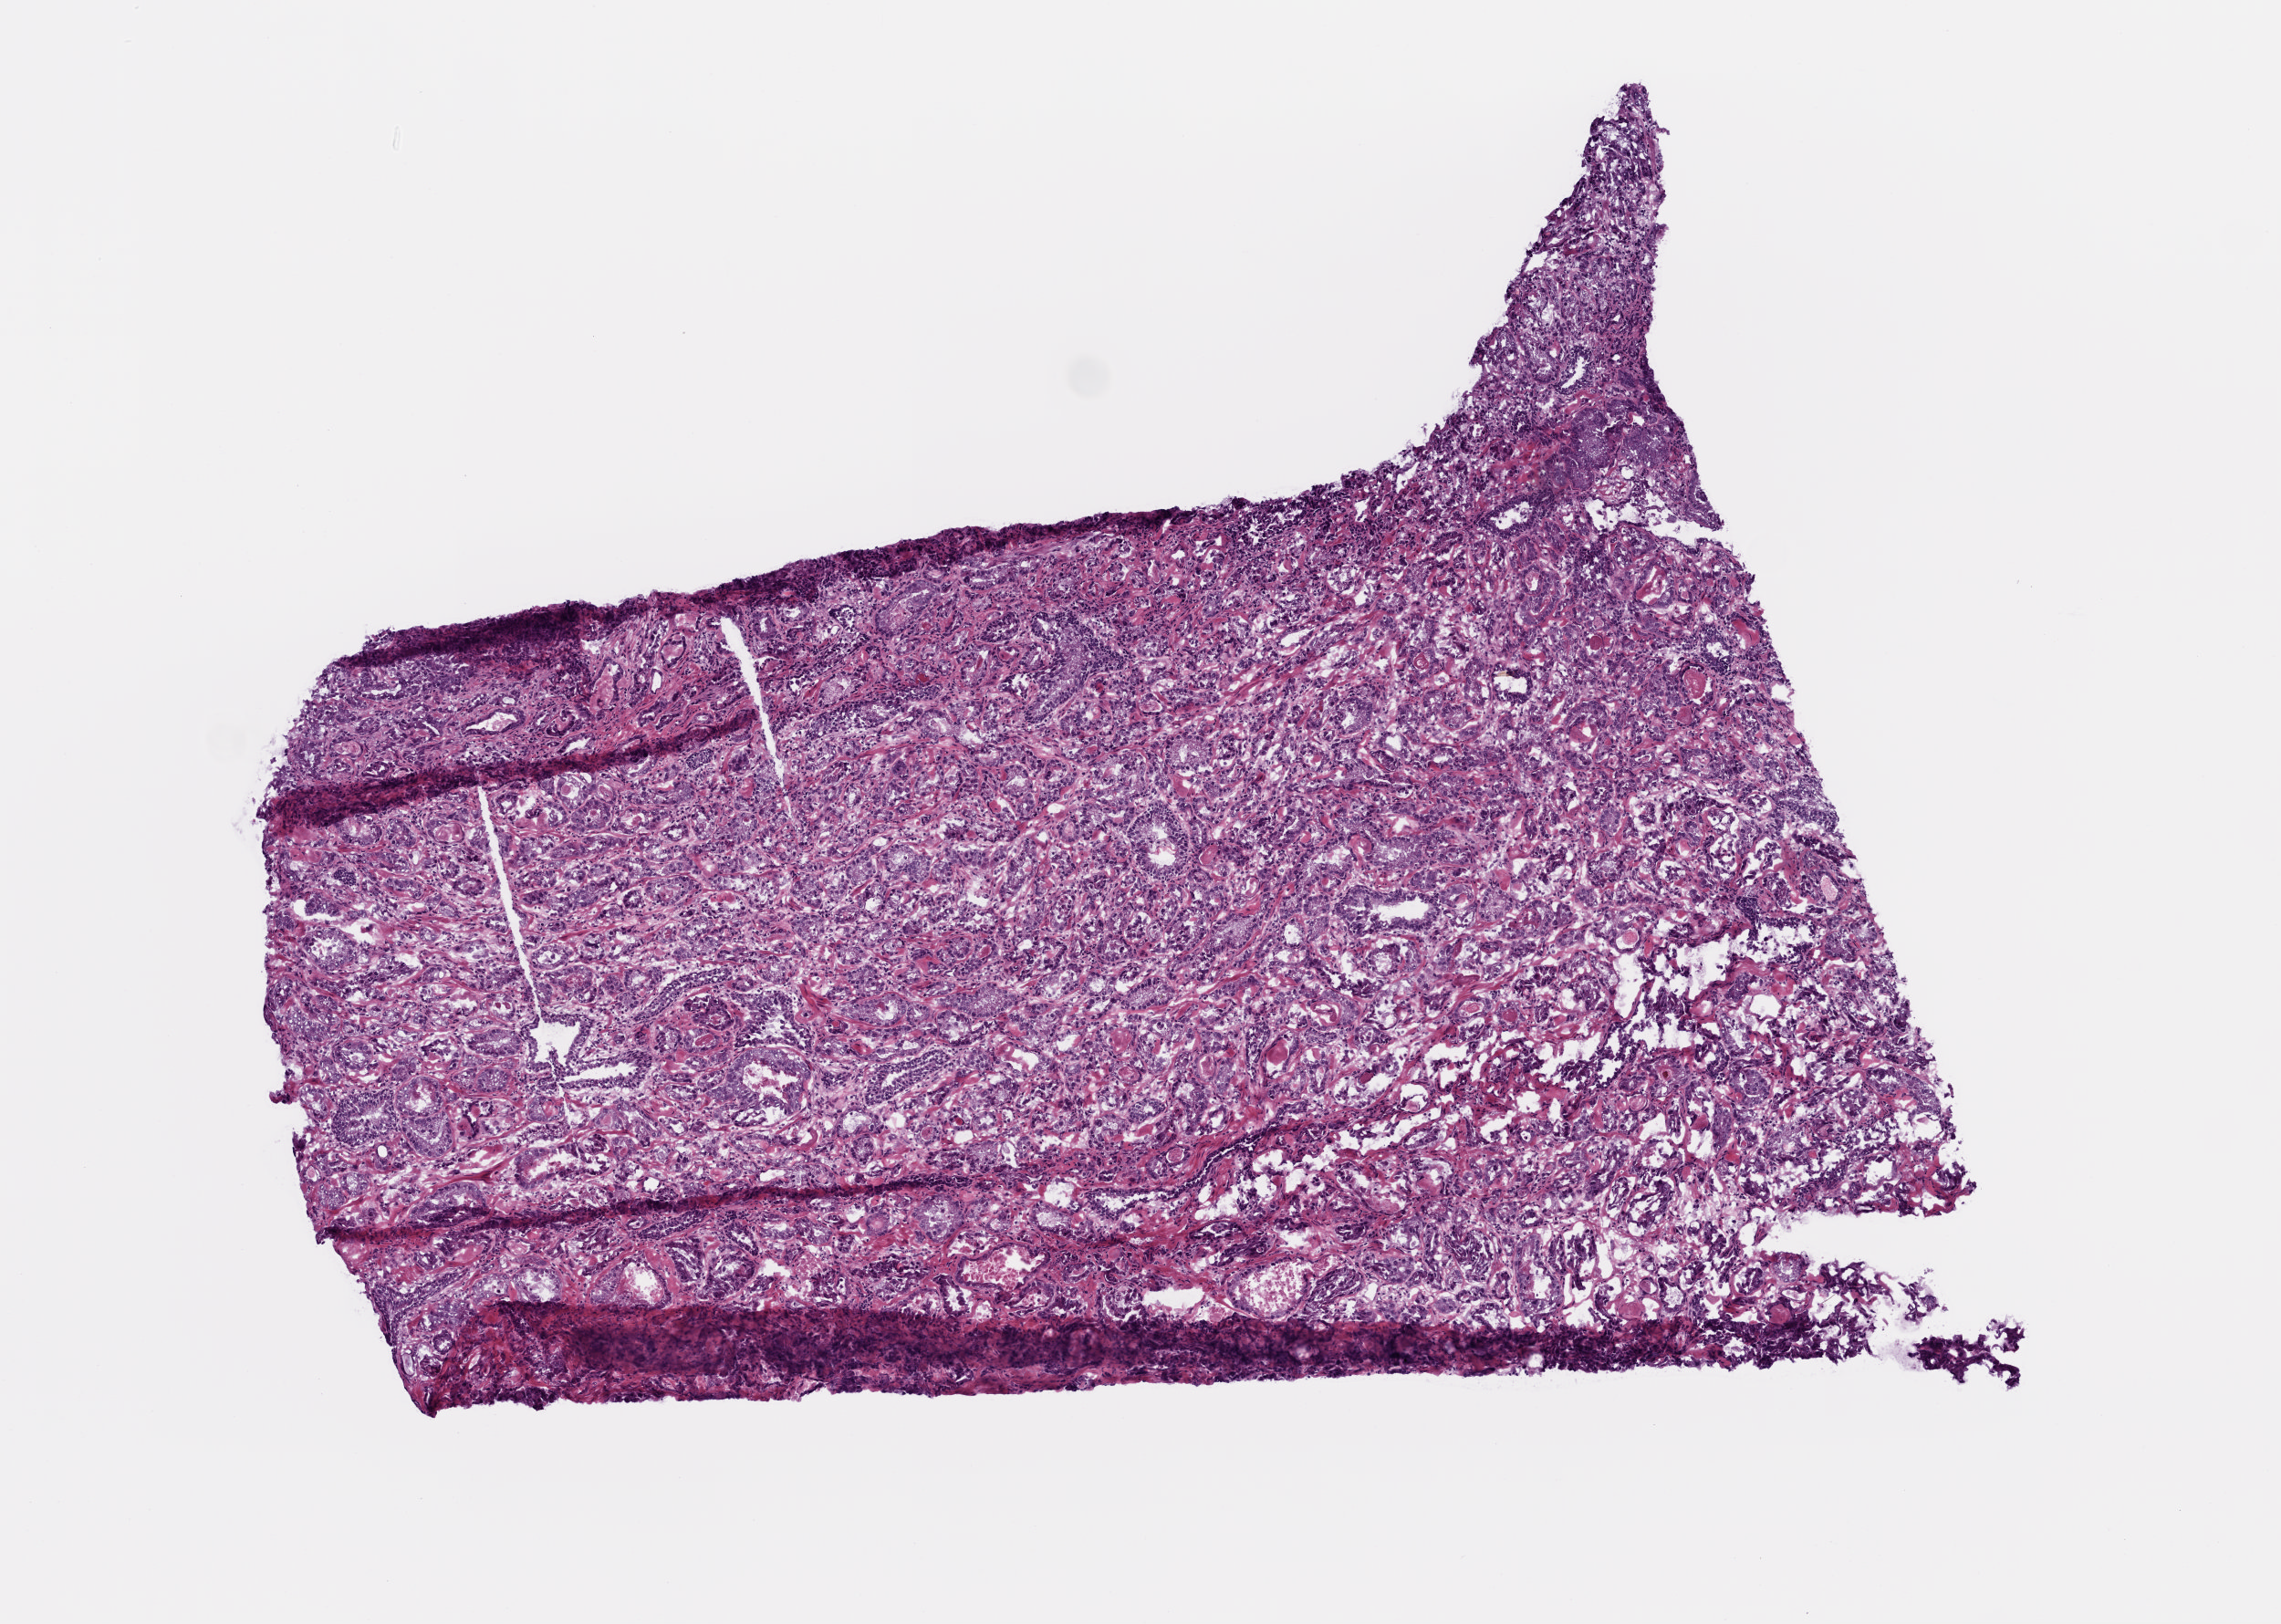
H&E-stained whole-slide image, shown as a low-resolution overview of the whole scanned area (about 5.0 x 3.6 mm, slide scanned at 20x); frozen section from the bottom of the tissue portion; primary tumour sample from the prostate. Male patient; age at initial diagnosis 55 years. Gleason score: 7 (4+3). Slide review estimates, as recorded: tumour cells 80%, tumour nuclei 80%, normal cells 12%, stromal cells 8%, necrosis 0%. Inflammatory infiltration, as recorded: lymphocyte infiltration 0%, monocyte infiltration 0%, neutrophil infiltration 0%.
Histologic diagnosis: Acinar cell carcinoma. Laterality: bilateral.